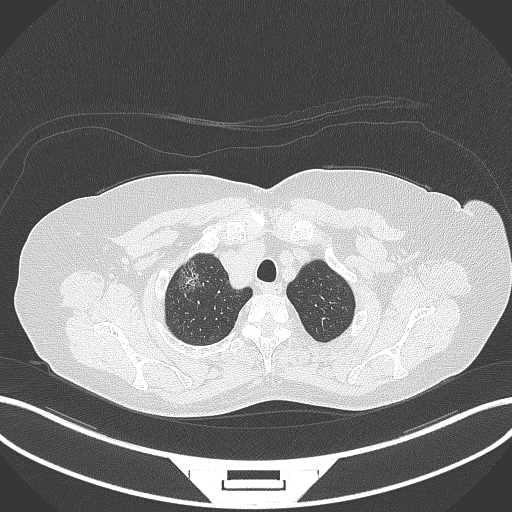
Chest CT, one axial slice. Position 310 of 365 along the scan axis. 120 kVp. Lung window (W 1500 / L -600 HU). 1 mm slice thickness. 512 × 512 image matrix. Female patient, age 62 years. From the clinical record (not read from this slice): clinical TNM (as recorded): T1c N0 M0.
Outlined on this slice (rectangle marked by the reading radiologist):
- lung tumour (recorded histology: adenocarcinoma): bounding box (x1, y1, x2, y2) in pixels: (177, 258, 208, 296)